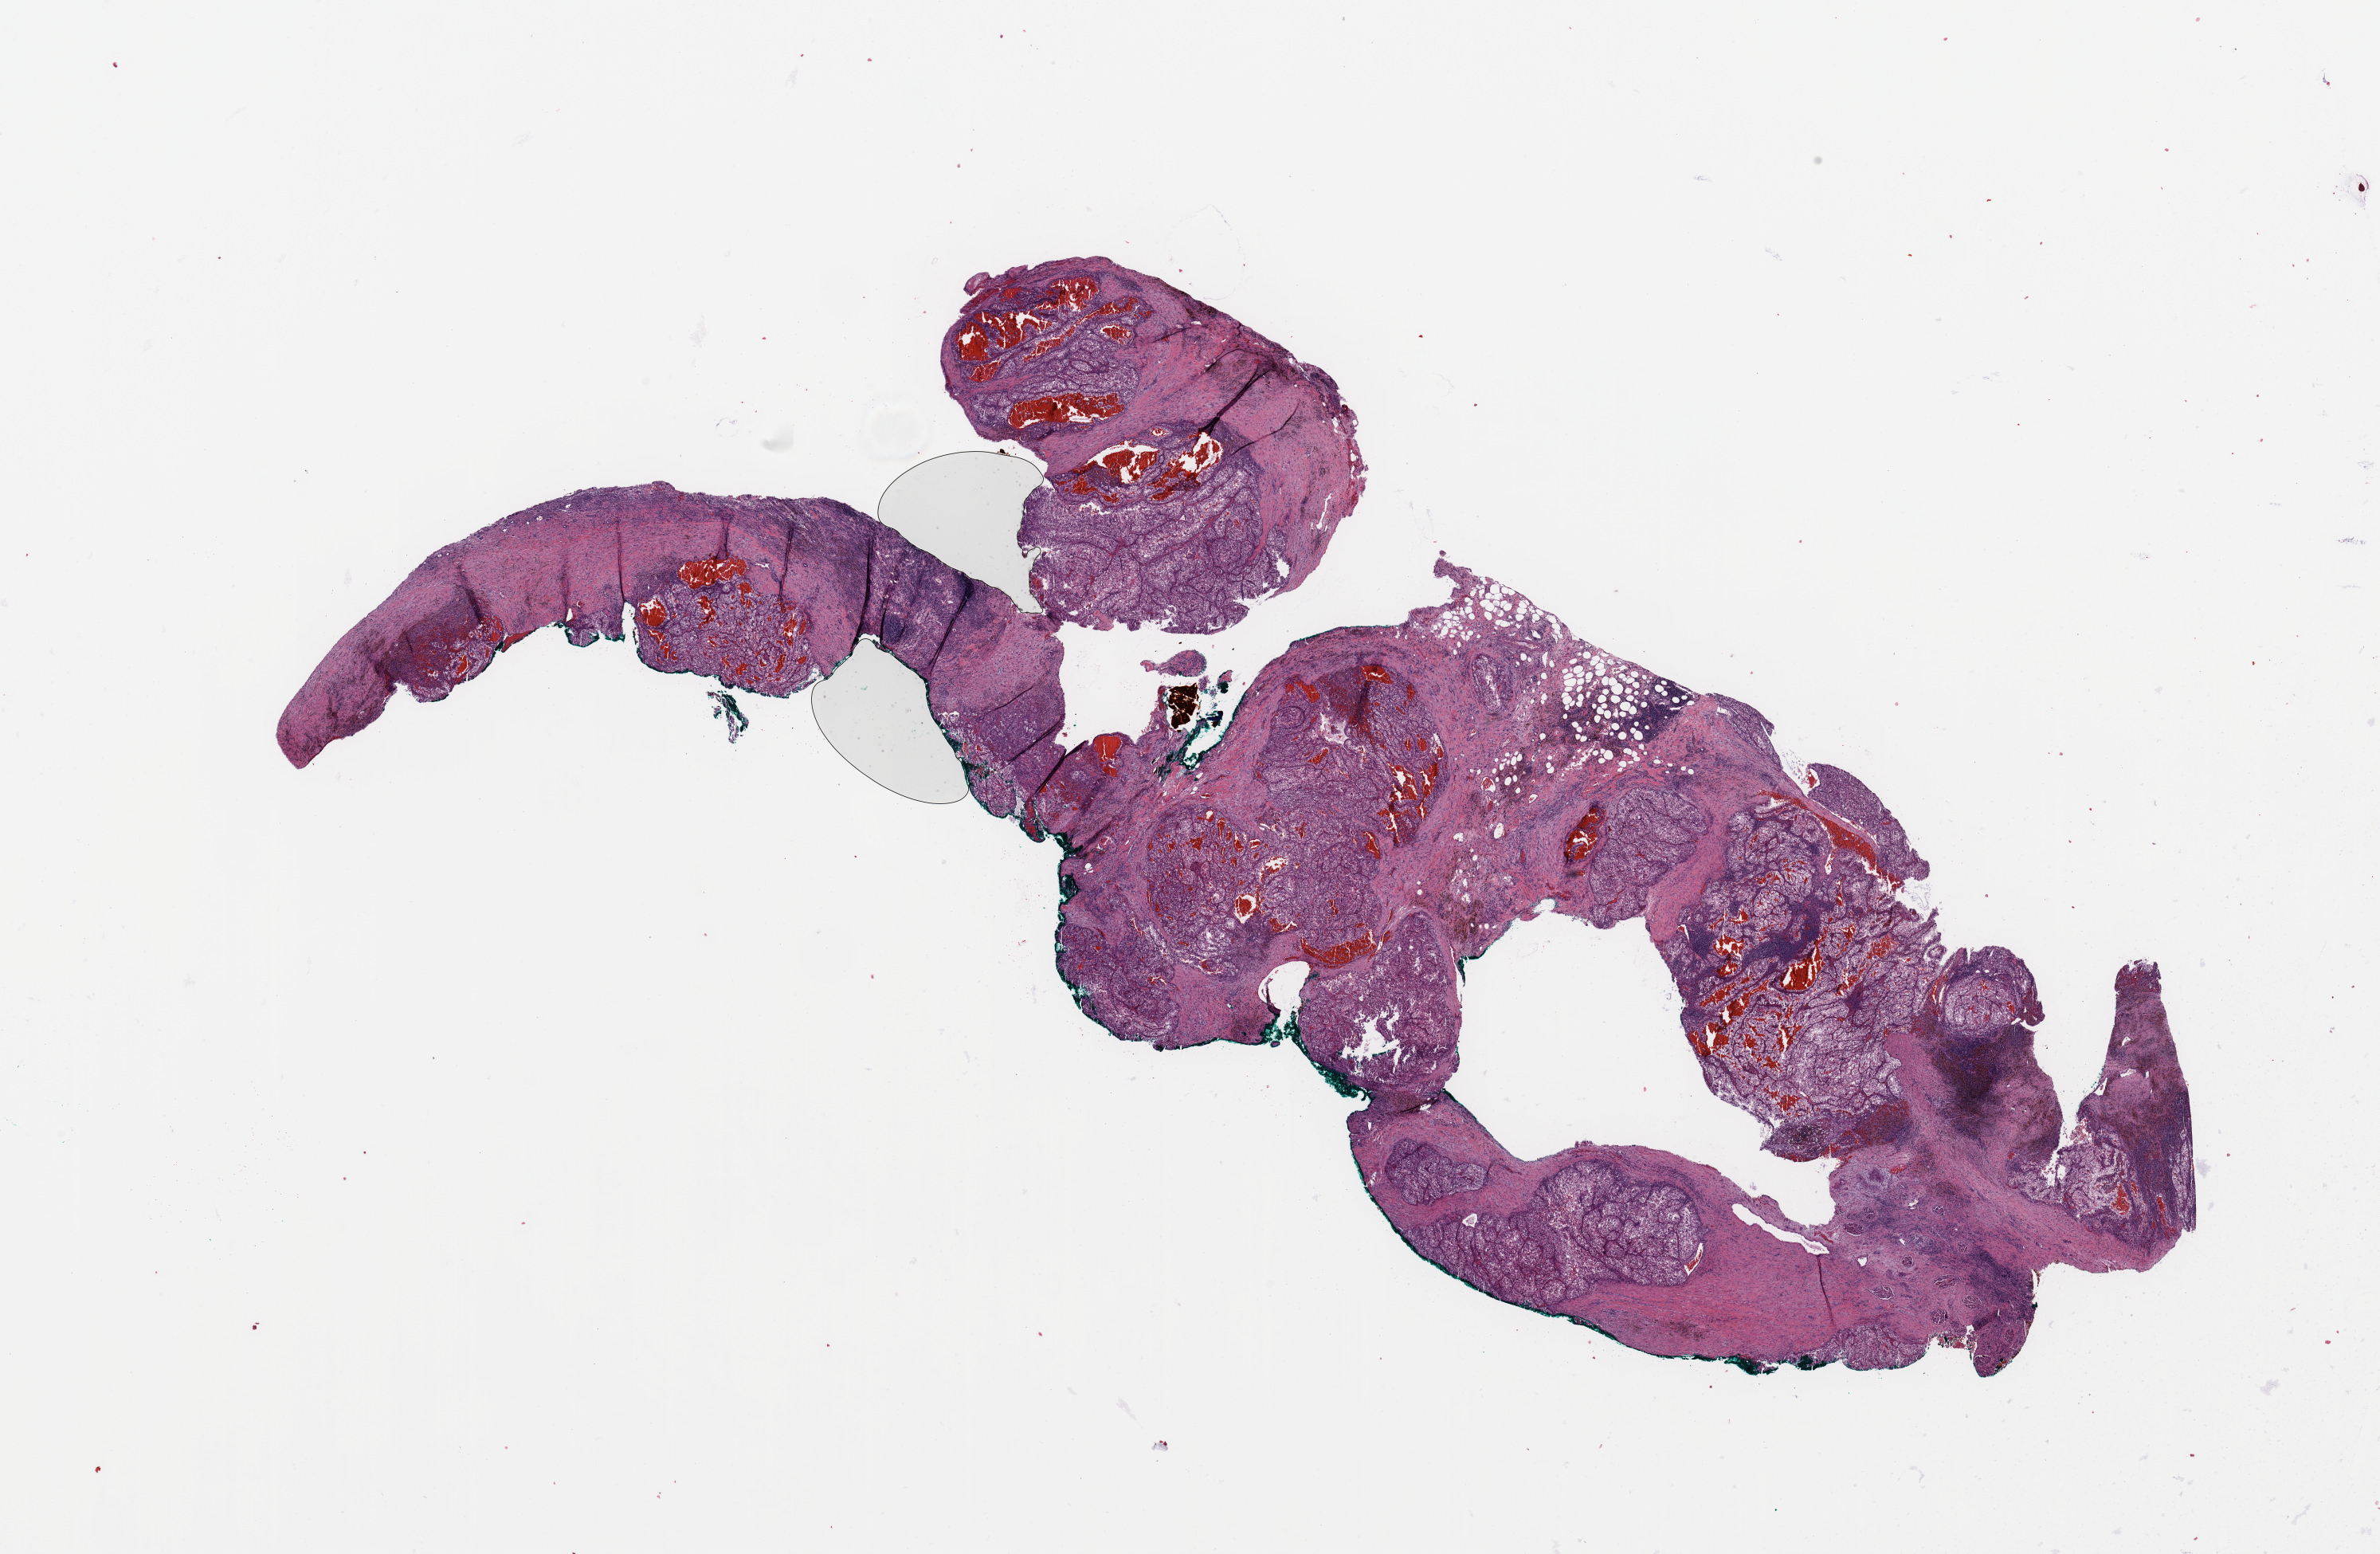
Whole-slide histology image, H&E-stained, shown as a low-resolution overview of the whole scanned area (about 23.6 x 15.4 mm), tumour tissue sample, sampled site: kidney. Male, 53 y/o. Histologic grade: G3 (poorly differentiated). Pathologist review of this section (percent, as recorded): tumour nuclei 80%, necrosis 0%.
* diagnosis: Renal cell carcinoma, NOS